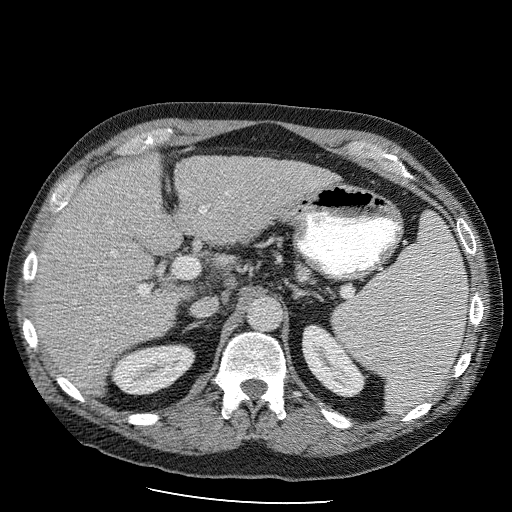
Contrast-enhanced abdominal CT (liver protocol), one axial slice; slice 59 of 98 in the series (ordered by position); soft-tissue window (W 400 / L 40 HU); 512 × 512 image matrix. Case-level facts recorded for this patient, not image findings: diagnosis: hepatocellular carcinoma (patient treated with transarterial chemoembolisation; whether this scan precedes or follows treatment is not stated here); TNM stage (as recorded): Stage-II.
Annotated regions visible in this slice (semi-automatic segmentation, software-assisted and operator-edited):
- liver parenchyma outside the tumour (the mass and vessels are separate outlines, so this box may not span the whole liver): bounding box <38,148,350,398> (left, top, right, bottom; pixels)
- liver vessels: <122,204,202,311>